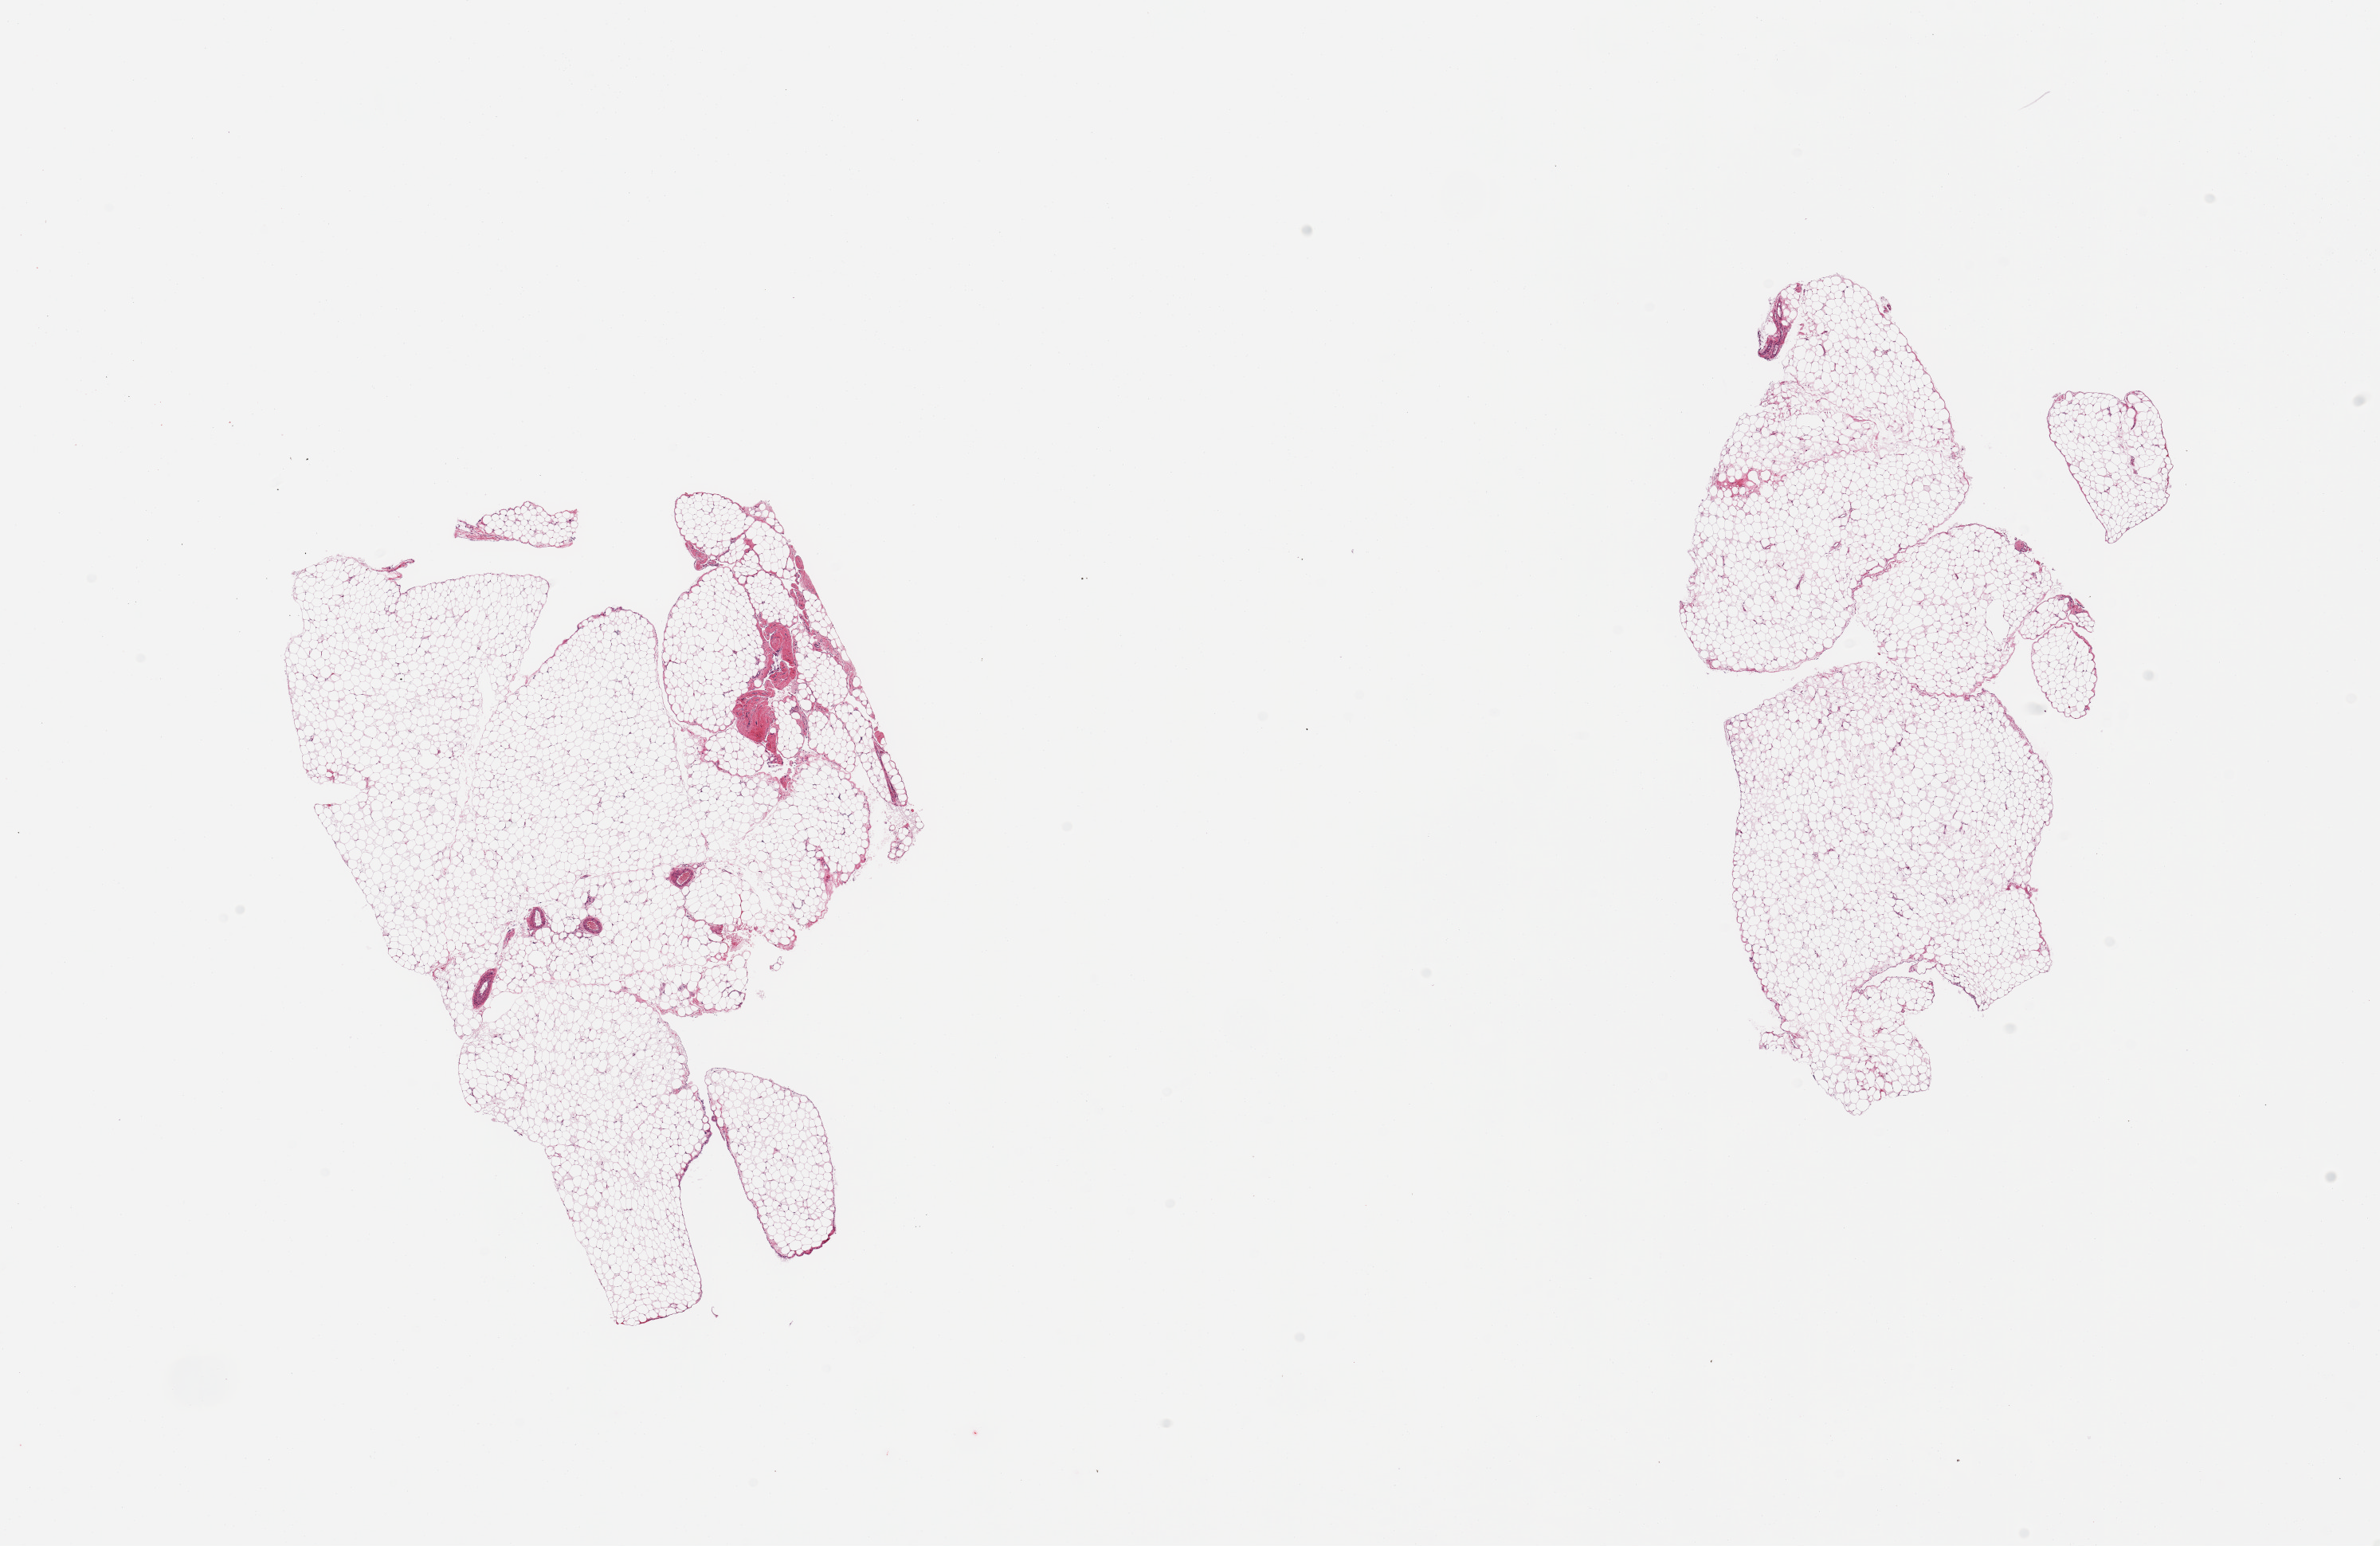
Whole-slide image, haematoxylin and eosin stain — shown as a low-resolution overview of the whole scanned area (about 23.6 x 15.3 mm, slide scanned at 20x); PAXgene-fixed, paraffin-embedded tissue; sampled site (target tissue): omentum; donor tissue sample. Male donor.
Reviewer comment on this tissue sample: 2 pieces; low stromal content.